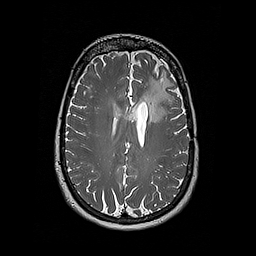
Brain MRI from a brain-tumour surgery series, one axial slice. Slice 119 of 192 in the series (ordered by position). 1 mm slice thickness. 256 × 256 image matrix. From the clinical record (not read from this slice): histopathology: Oligodendroglioma; WHO grade: 2; IDH mutation: yes; tumour location: Left Frontal.
Structures marked on this image (expert manual segmentation):
- tumour: bounding box [x1, y1, x2, y2] px = [142, 77, 171, 122]